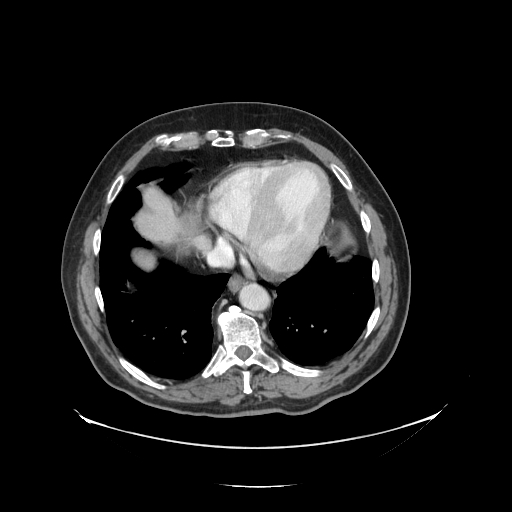
Contrast-enhanced abdominal CT, one axial slice. Slice 123 of 138 in the series (ordered by position). Reconstruction kernel STANDARD. 120 kVp. Intravenous contrast given. Soft-tissue window (W 400 / L 40 HU). 512 × 512 image matrix, field of view 497 × 497 mm. Male patient, age 77 years. Case-level facts recorded for this patient, not image findings: diagnosis: colorectal cancer liver metastases, imaged before liver resection; multiple liver metastases: no.
Structures marked on this image (manually delineated by an expert):
- liver: box from (x=136, y=188) to (x=182, y=268) px
- planned liver remnant (the part of the liver to remain after resection): (x=135, y=189)–(x=182, y=269)